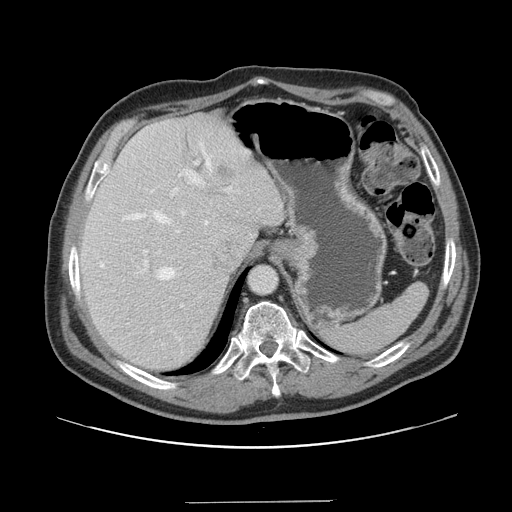
Contrast-enhanced abdominal CT, one axial slice; slice 115 of 151 in the series (ordered by position); soft-tissue window (W 400 / L 40 HU); 2.5 mm slice thickness; 512 × 512 image matrix. Male patient, age 63 years. Case-level facts recorded for this patient, not image findings: diagnosis: colorectal cancer liver metastases, imaged before liver resection; multiple liver metastases: no; largest metastasis: 2.1 cm; disease in both lobes: no.
Structures marked on this image (manually delineated by an expert):
- hepatic veins: bounding box <100,143,212,280> (left, top, right, bottom; pixels)
- liver: <79,113,284,372>
- planned liver remnant (the part of the liver to remain after resection): <79,118,262,372>
- portal vein (with intrahepatic branches): <140,161,232,306>
- liver metastasis: <218,168,235,182>